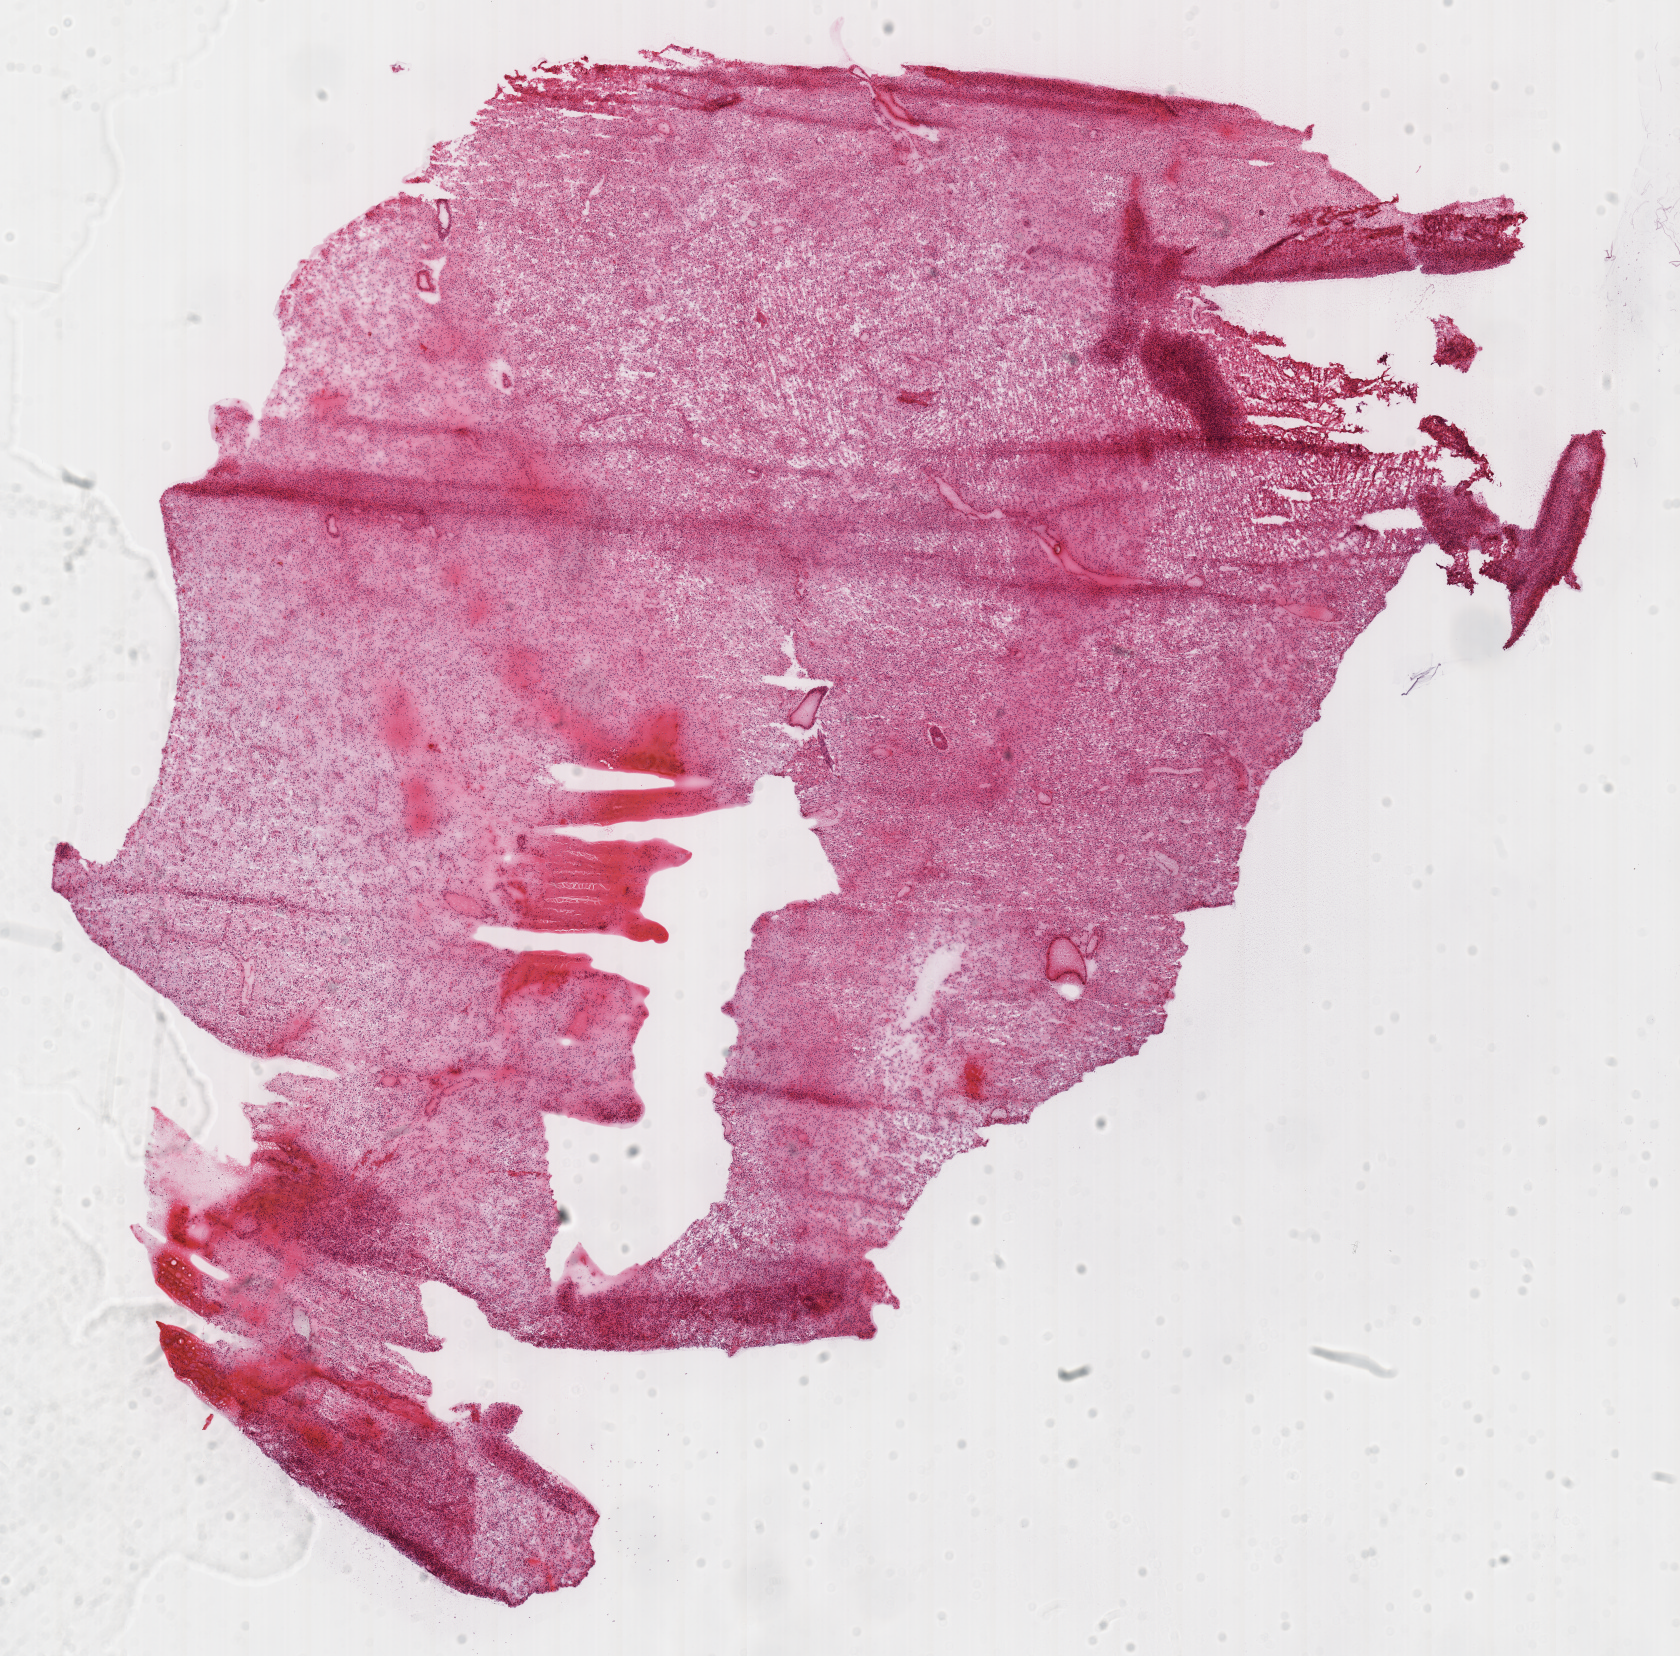
Whole-slide histology image, H&E-stained — shown as a low-resolution overview of the whole scanned area (about 13.2 x 13.0 mm, from a 40x scan). Frozen section from the top of the tissue portion. Brain, primary tumour sample. Male patient; age at initial diagnosis 31 years. Histologic grade: G3 (poorly differentiated). Pathologist review of this section (percent, as recorded): tumour cells 100%, tumour nuclei 85%, normal cells 0%, stromal cells 0%, necrosis 0%.
Pathologic diagnosis: Astrocytoma, NOS (cerebrum).